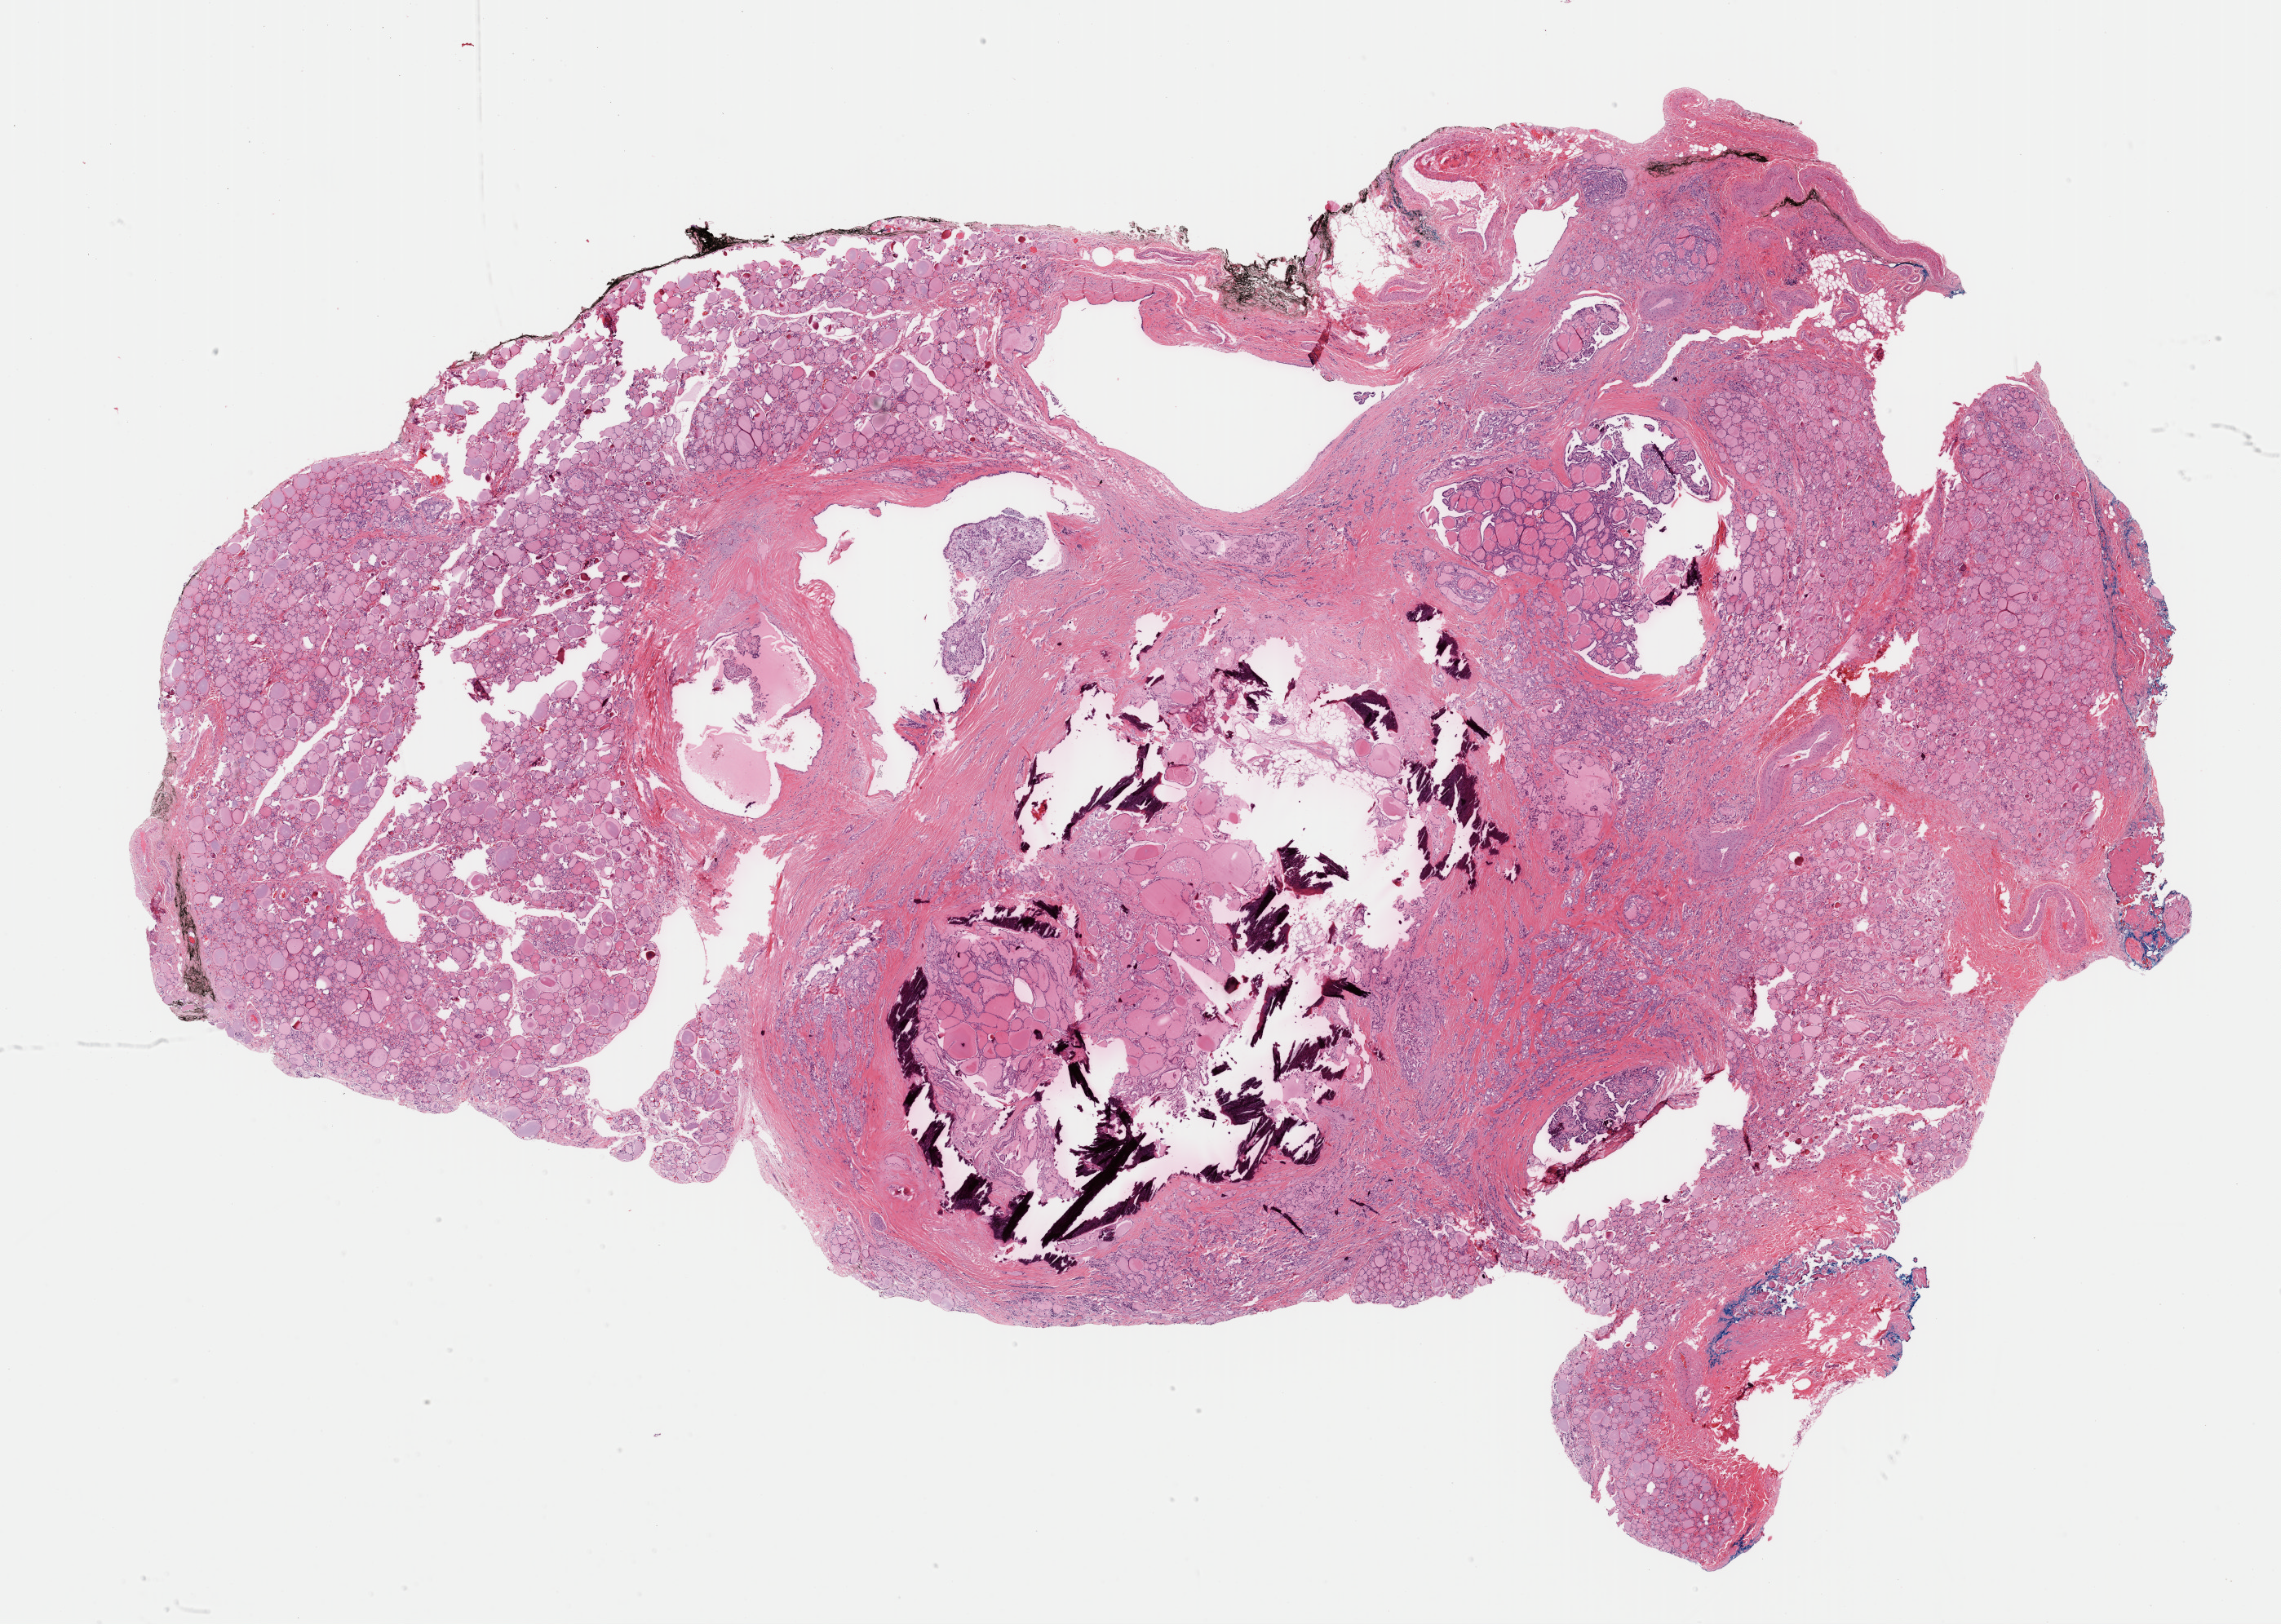
Whole-slide histology image, H&E-stained — low-resolution overview of the scanned area, about 22.1 x 15.7 mm (acquisition: 40x scan); FFPE section; primary tumour sample from the thyroid. Female patient; age at initial diagnosis 55 years.
Diagnosis: Papillary adenocarcinoma, NOS (thyroid gland). Lymph nodes positive (case pathology): 2 of 14 examined. Laterality: right. AJCC pathologic stage: III (5th edition). TNM: T2 N1 M0.